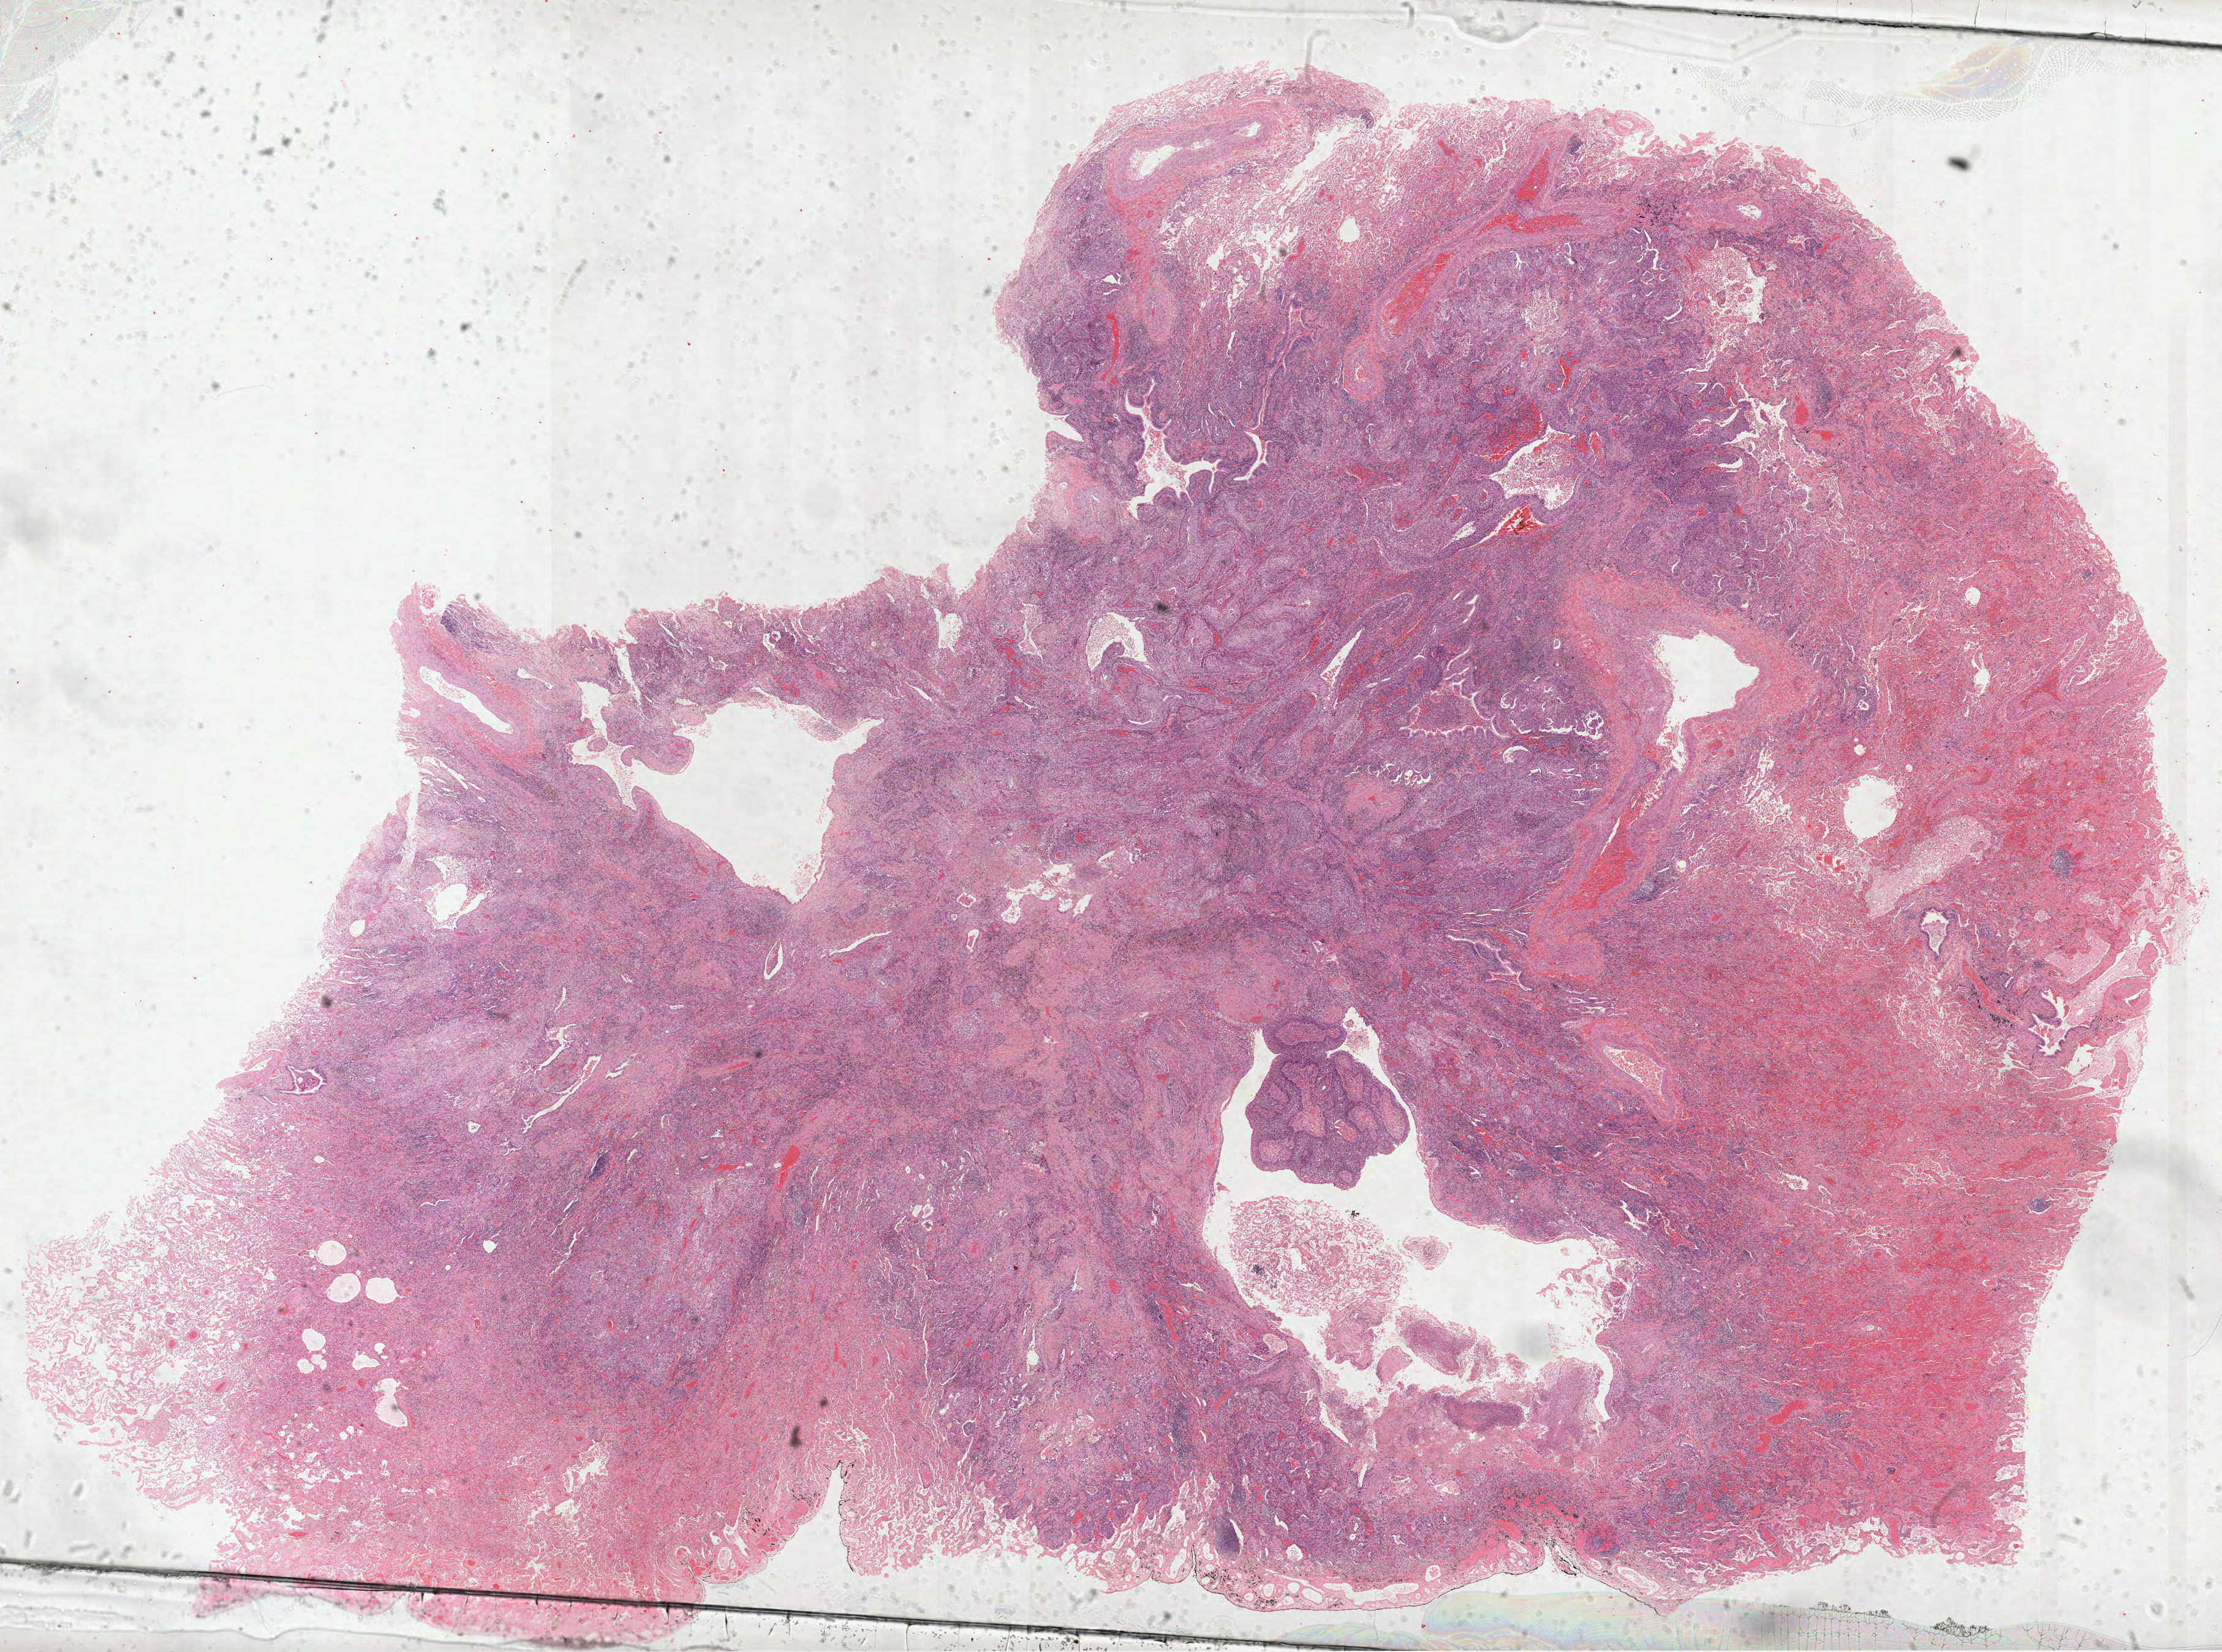
Digitized H&E tissue section (whole slide) — whole scanned area (about 29.2 x 21.7 mm, from a 40x scan) shown as a low-resolution overview; FFPE section; primary tumour sample from the lung. Patient: male, age at initial diagnosis 72 years.
AJCC pathologic stage: IA (6th edition). Pathologic diagnosis: Squamous cell carcinoma, NOS (upper lobe, lung). TNM: T1 N0 M0.